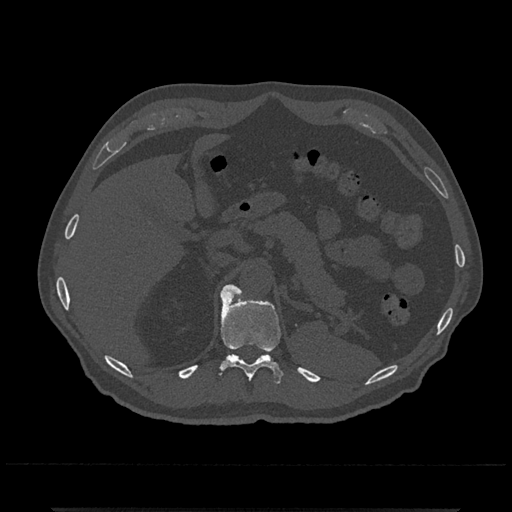
CT including the spine, one axial slice. Position 485 of 797 along the scan axis. Reconstruction kernel Br40s/3. 120 kVp. Bone window (W 1800 / L 400 HU). 0.5 mm slice thickness. 512 × 512 image matrix, field of view 393 × 393 mm. Male patient, age 67 years. Case-level facts recorded for this patient, not image findings: primary cancer: prostate.
Annotated regions visible in this slice (semi-automatic segmentation, software-assisted and operator-edited):
- T11 vertebra: bounding box (x1, y1, x2, y2) in pixels: (220, 291, 282, 384)
- T12 vertebra: (221, 284, 242, 296)